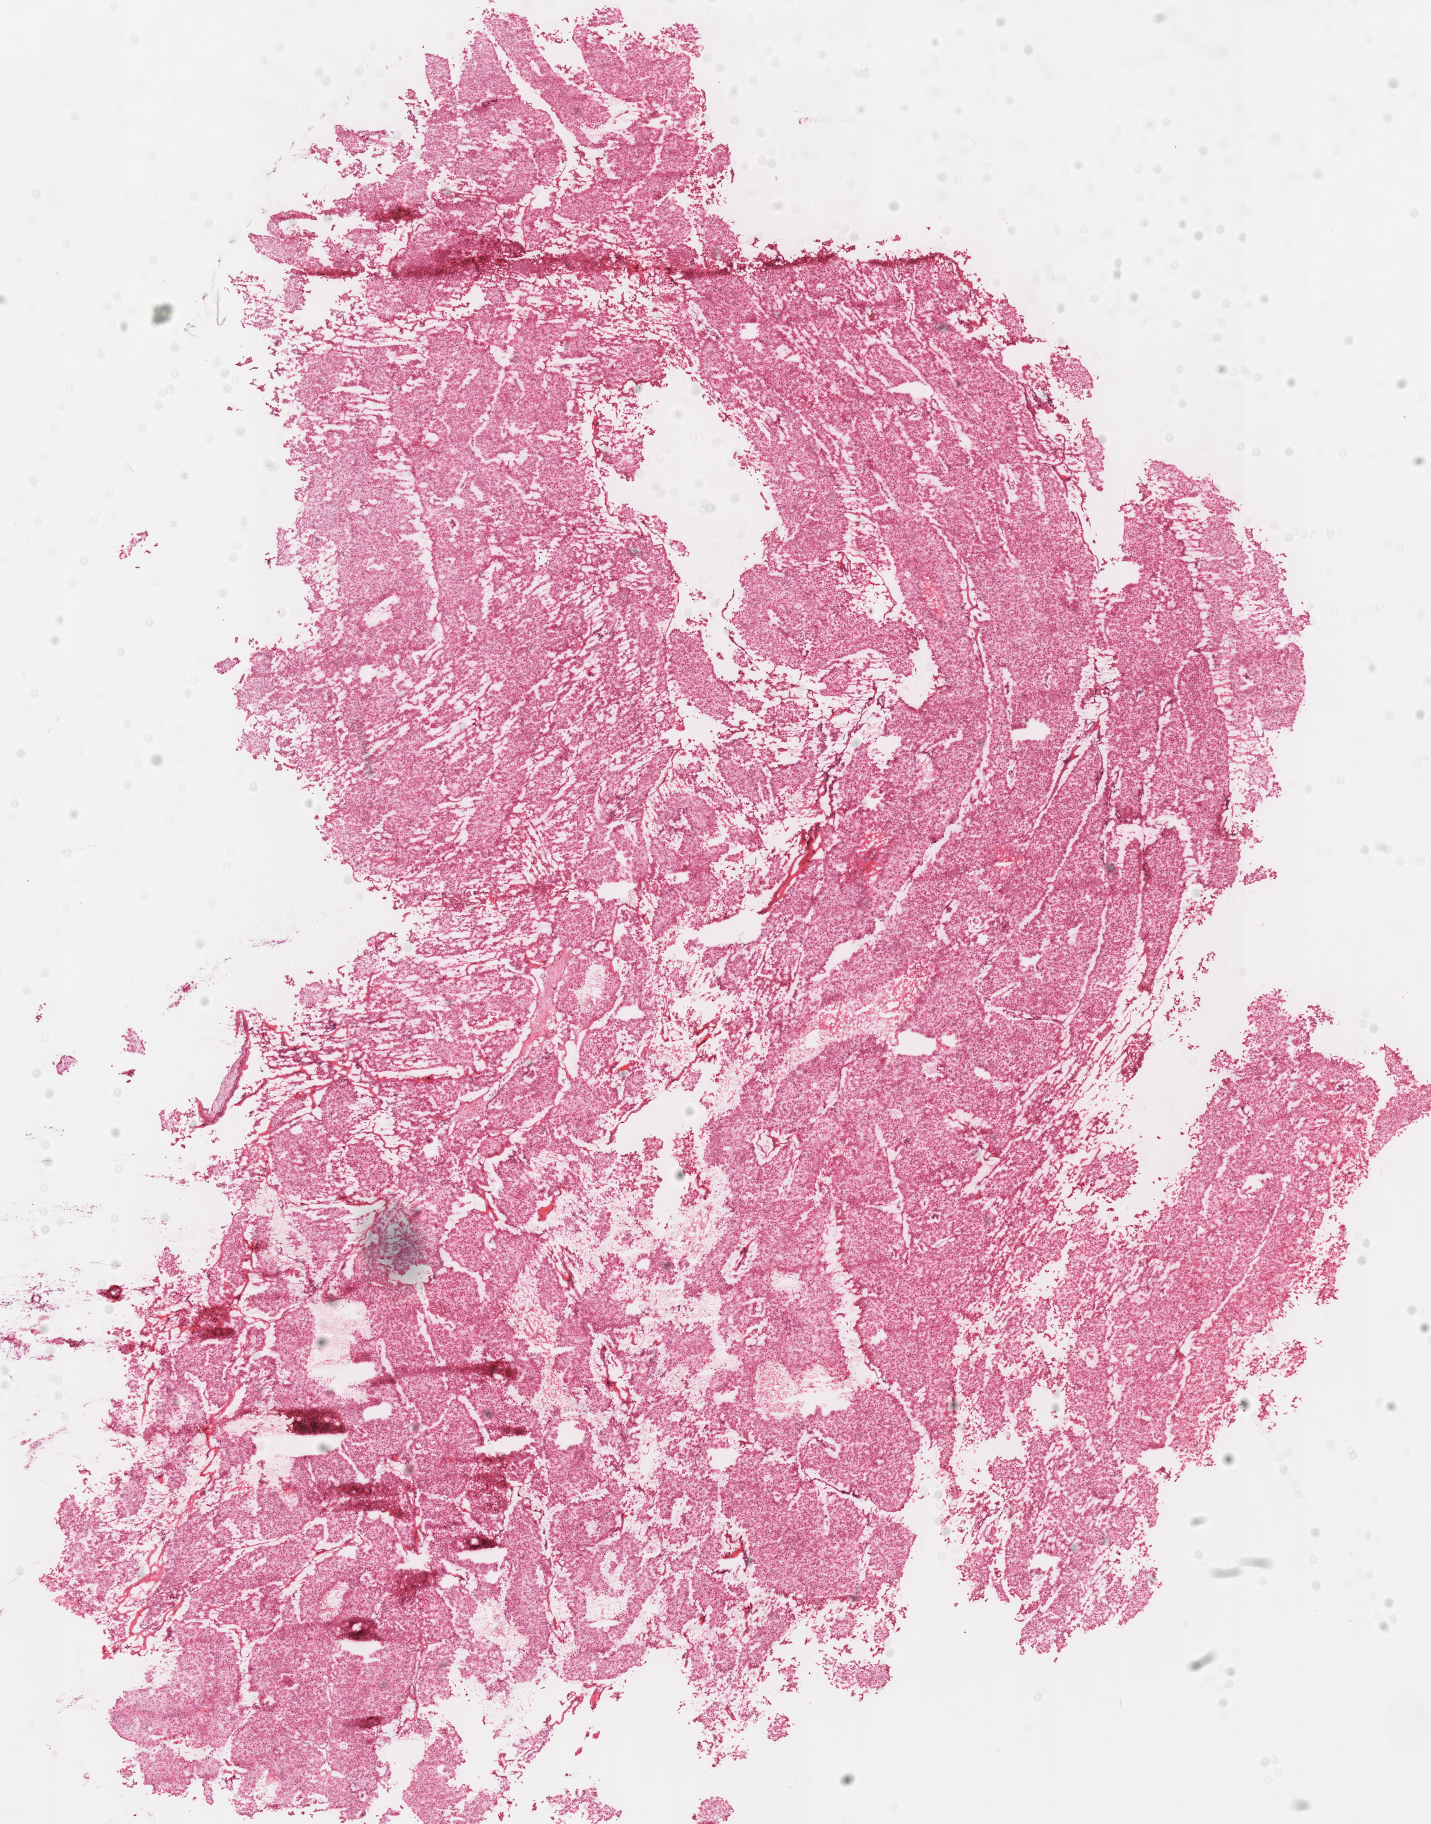
Whole-slide histology image, Hematoxylin and eosin (H&E) stained — low-resolution overview of the scanned area, about 11.3 x 14.3 mm (from a 40x scan); frozen section from the top of the tissue portion; primary tumour sample from the kidney. Male patient; age at initial diagnosis 59 years. Slide review estimates, as recorded: tumour cells 100%, tumour nuclei 95%.
Histologic diagnosis: Renal cell carcinoma, chromophobe type.